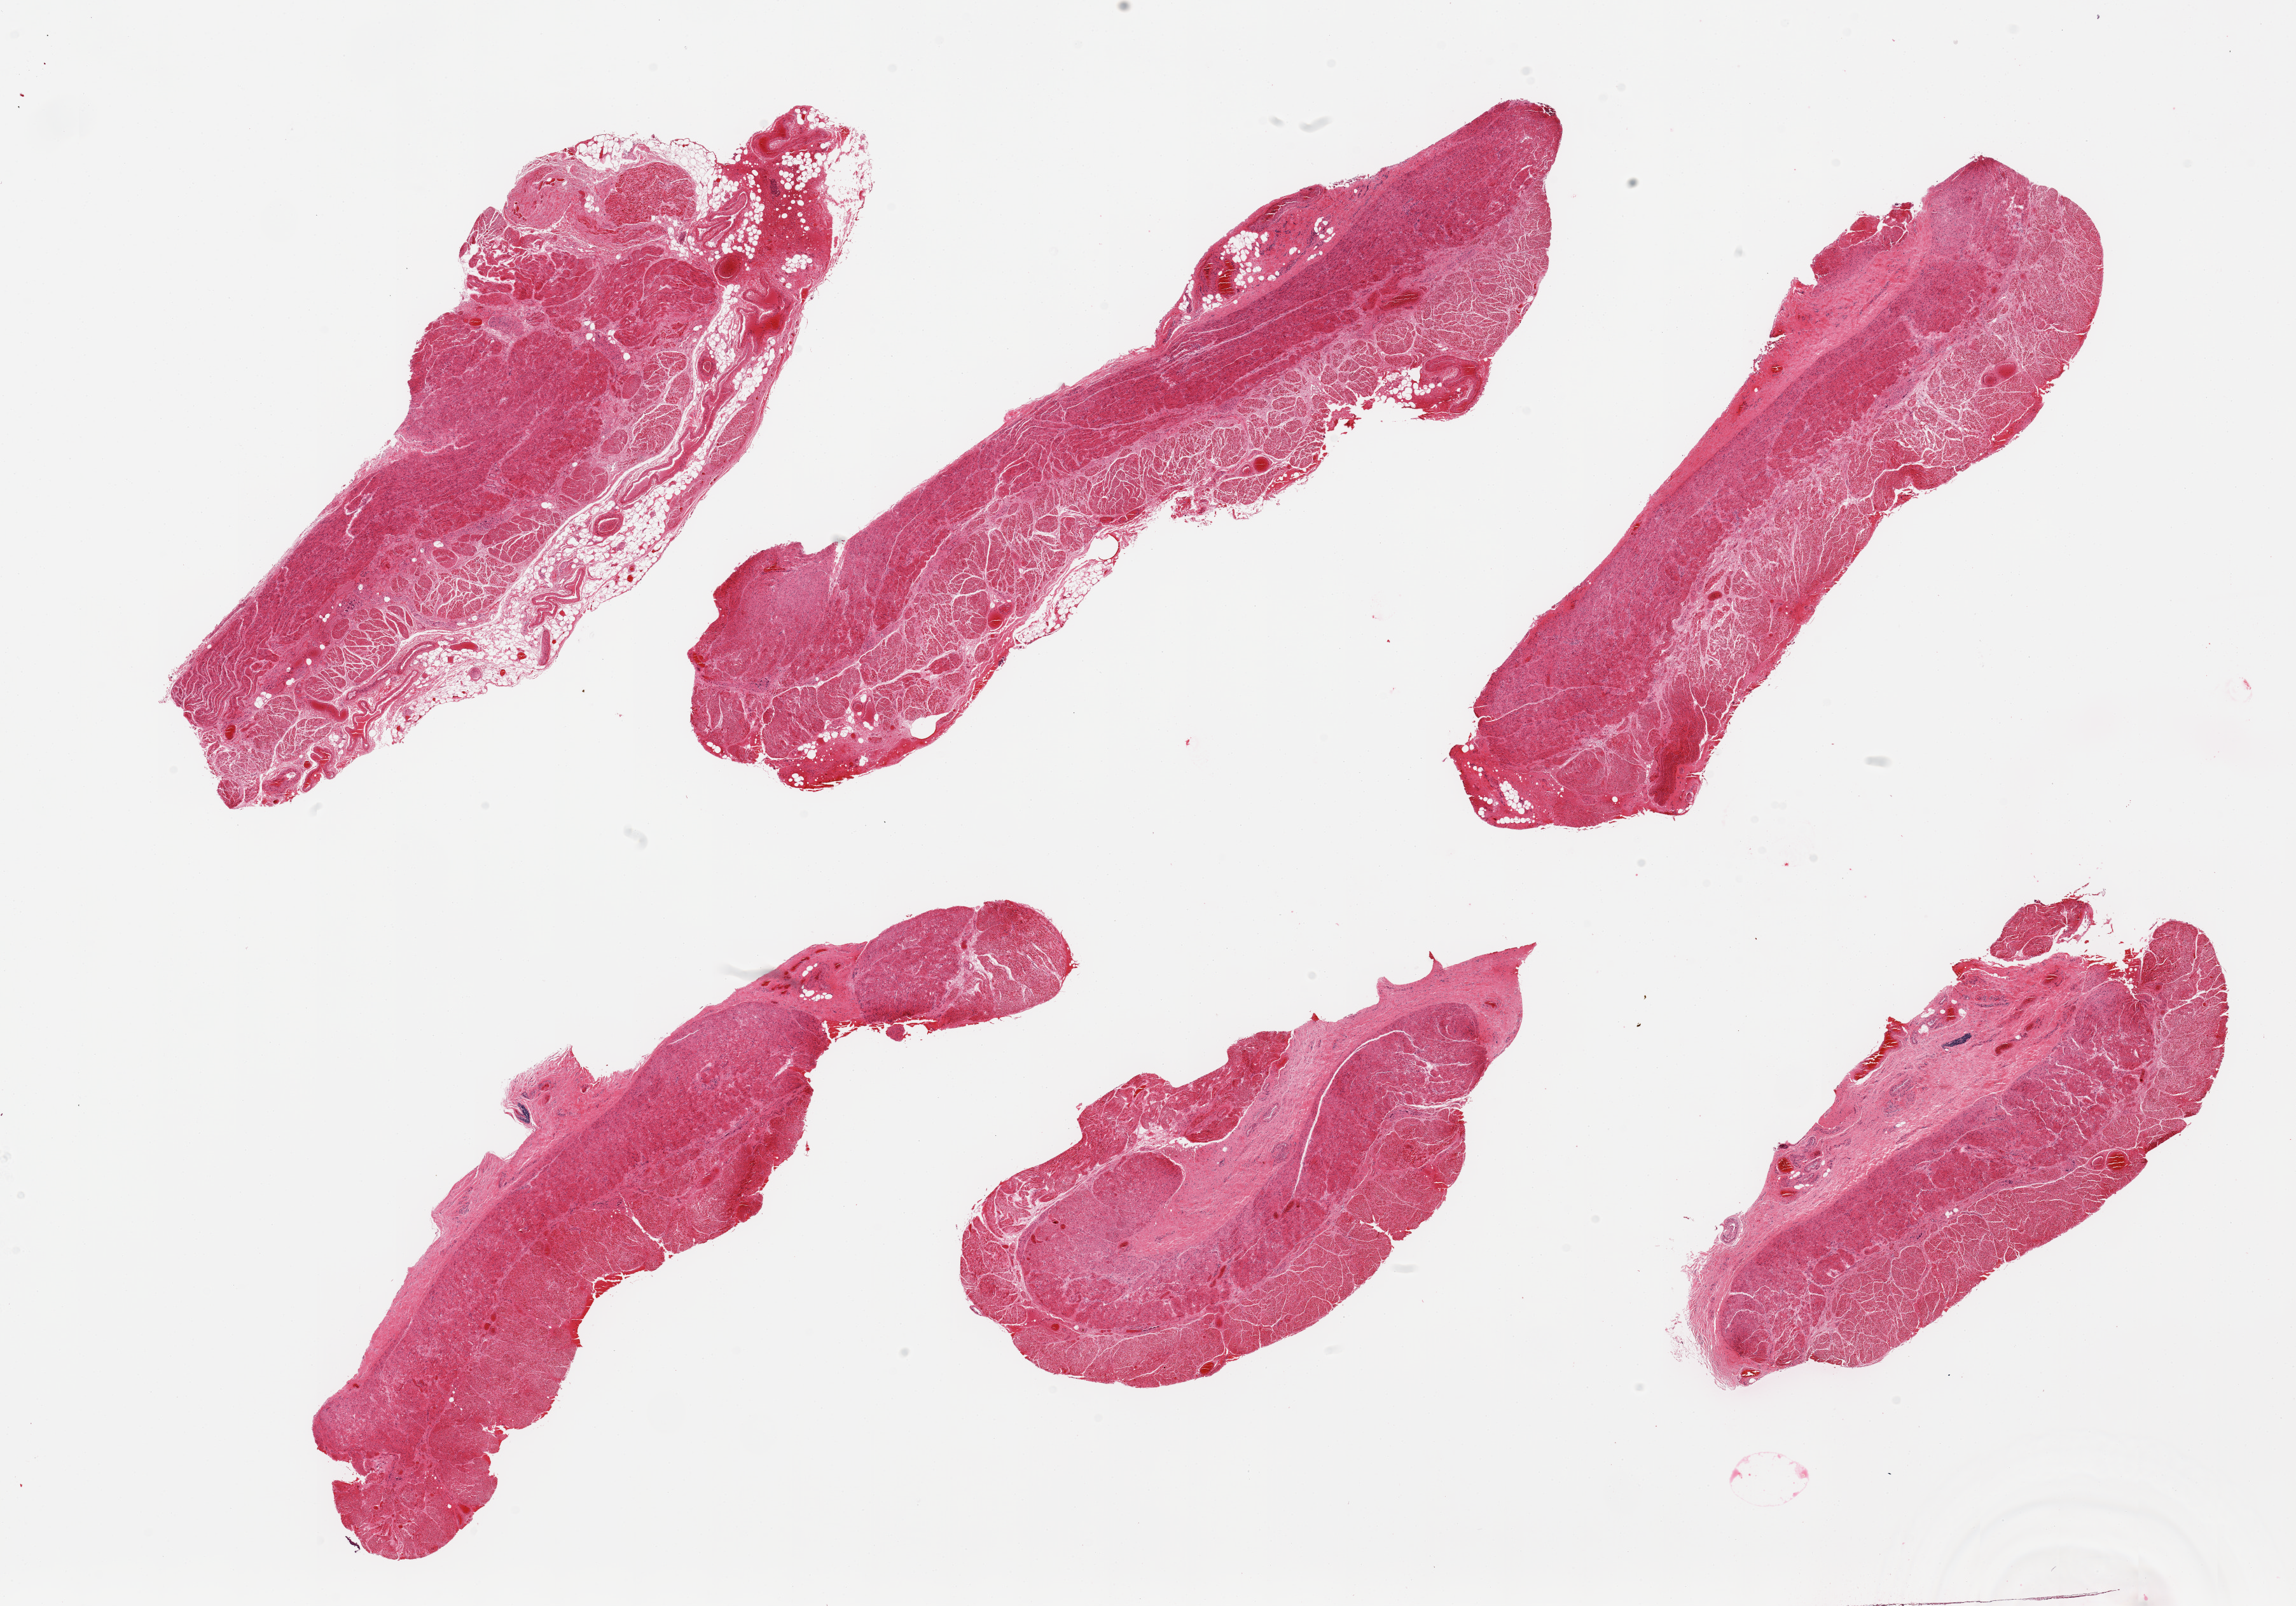
Digitized haematoxylin and eosin-stained section, brightfield, whole scanned area (about 28.5 x 20.0 mm) shown as a low-resolution overview, PAXgene-fixed paraffin-embedded (PFPE) section, section of gastroesophageal junction (target tissue), tissue donor sample. Donor sex: male.
• reviewer comment on this tissue sample: 6 pieces; 1 has 1 mm perimuscular fat